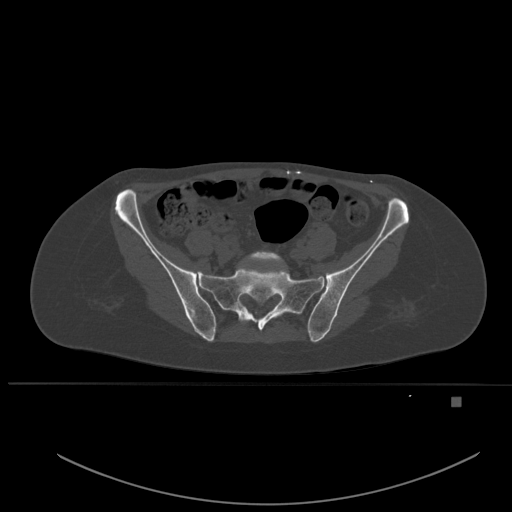
CT including the spine, one axial slice. Slice 138 of 651 in the series (ordered by position). Bone window (W 1800 / L 400 HU). 512 × 512 image matrix. Patient: female, 49 years. From the clinical record (not read from this slice): primary cancer: breast; vertebrae with lytic lesions (as recorded): L3, T12, L4.
Structures marked on this image (semi-automatic segmentation, software-assisted and operator-edited):
- L5 vertebra: bounding box (x1, y1, x2, y2) in pixels: (234, 251, 283, 276)